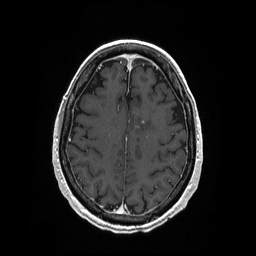
Brain MRI from a brain-tumour surgery series, one axial slice. Slice 70 of 208 in the series (ordered by position). T1-weighted post-contrast. 256 × 256 image matrix, field of view 256 × 256 mm. From the clinical record (not read from this slice): histopathology: Primary diffuse large B-cell lymphoma; tumour location: Left Corpus Callosum (Frontal).
Structures marked on this image (manually delineated by an expert):
- tumour: bounding box (x1, y1, x2, y2) in pixels: (137, 121, 145, 125)